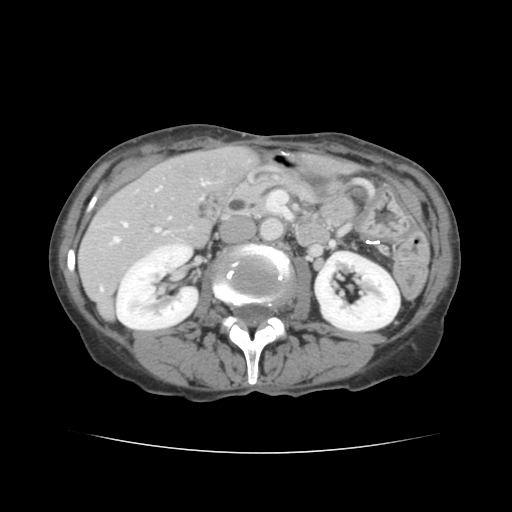
Contrast-enhanced abdominal CT, one axial slice; position 58 of 136 along the scan axis; soft-tissue window (W 400 / L 40 HU); 512 × 512 image matrix, field of view 319 × 319 mm. Female patient, age 77 years. Case-level facts recorded for this patient, not image findings: diagnosis: colorectal cancer liver metastases, imaged before liver resection.
Annotated regions visible in this slice (outlined manually by an expert reader):
- hepatic veins: bounding box (x1, y1, x2, y2) in pixels: (114, 181, 206, 242)
- liver: (80, 146, 256, 317)
- planned liver remnant (the part of the liver to remain after resection): (165, 146, 257, 198)
- portal vein (with intrahepatic branches): (100, 182, 209, 291)